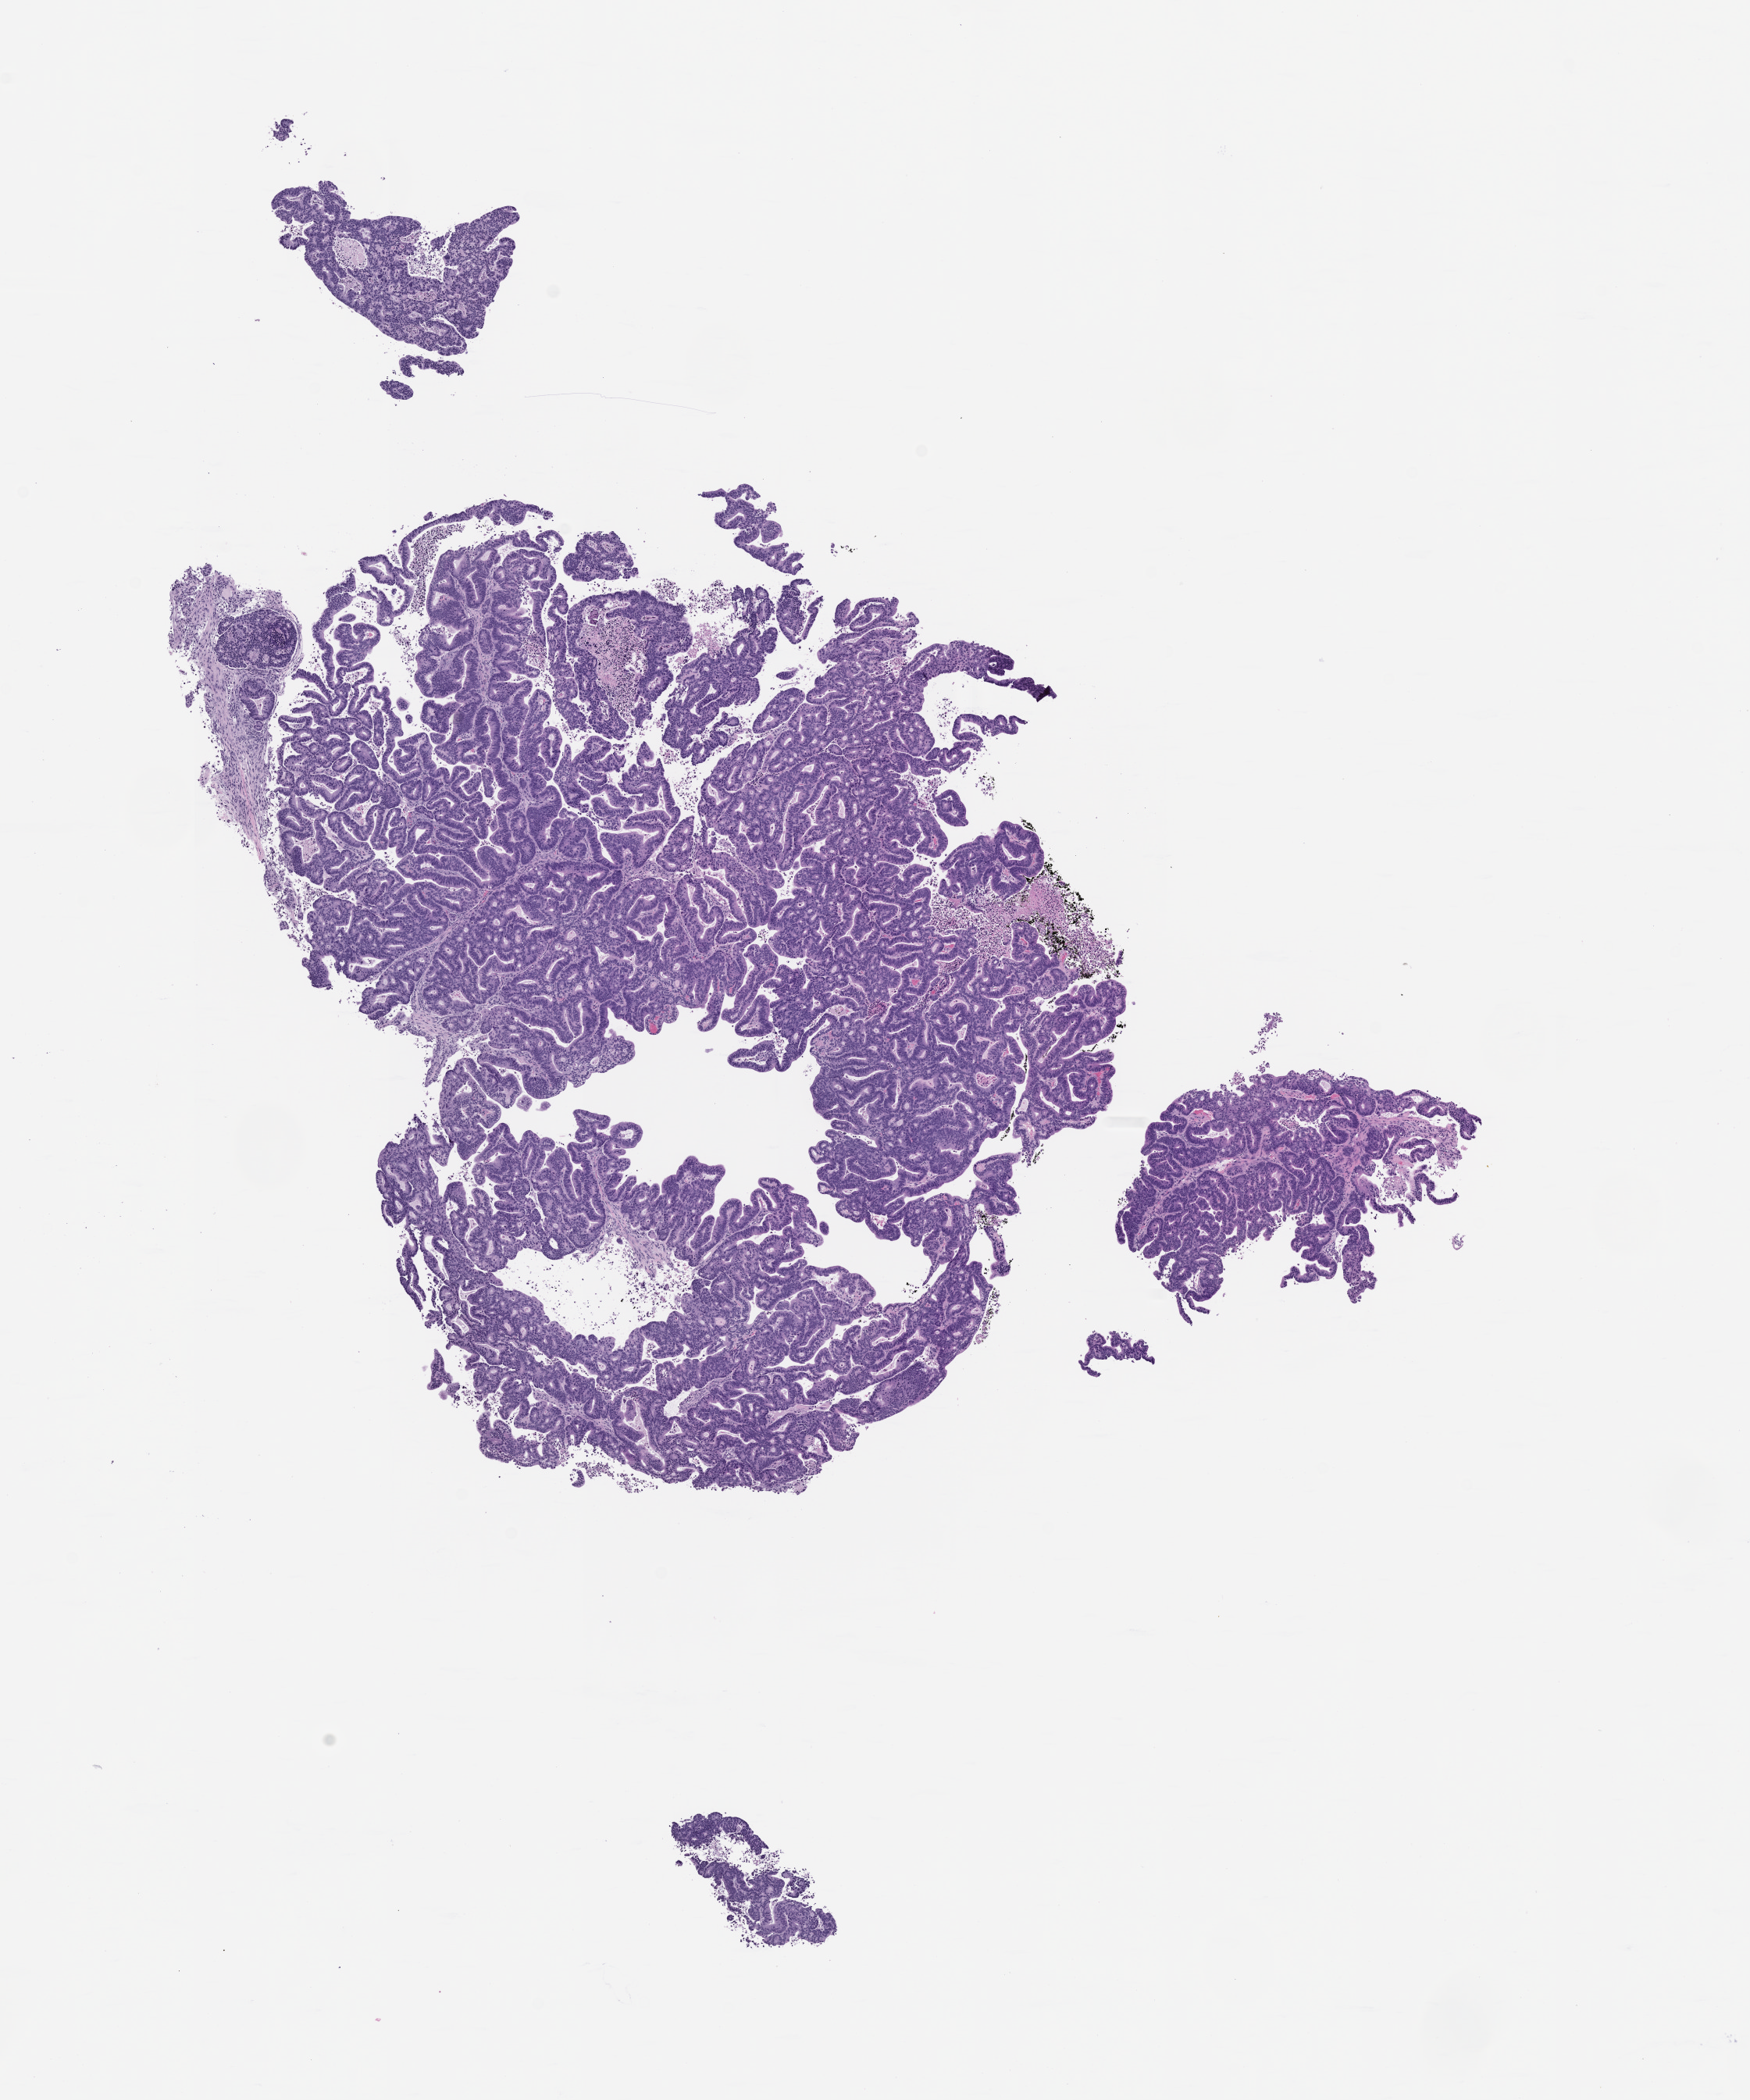
H&E whole-slide image of a patient-derived xenograft (PDX) tumor grown in a mouse, passage 0, whole scanned area (about 9.0 x 10.8 mm) shown as a low-resolution overview, FFPE section, originating tumor site category: colon.
- originating patient diagnosis: Colon Adenocarcinoma